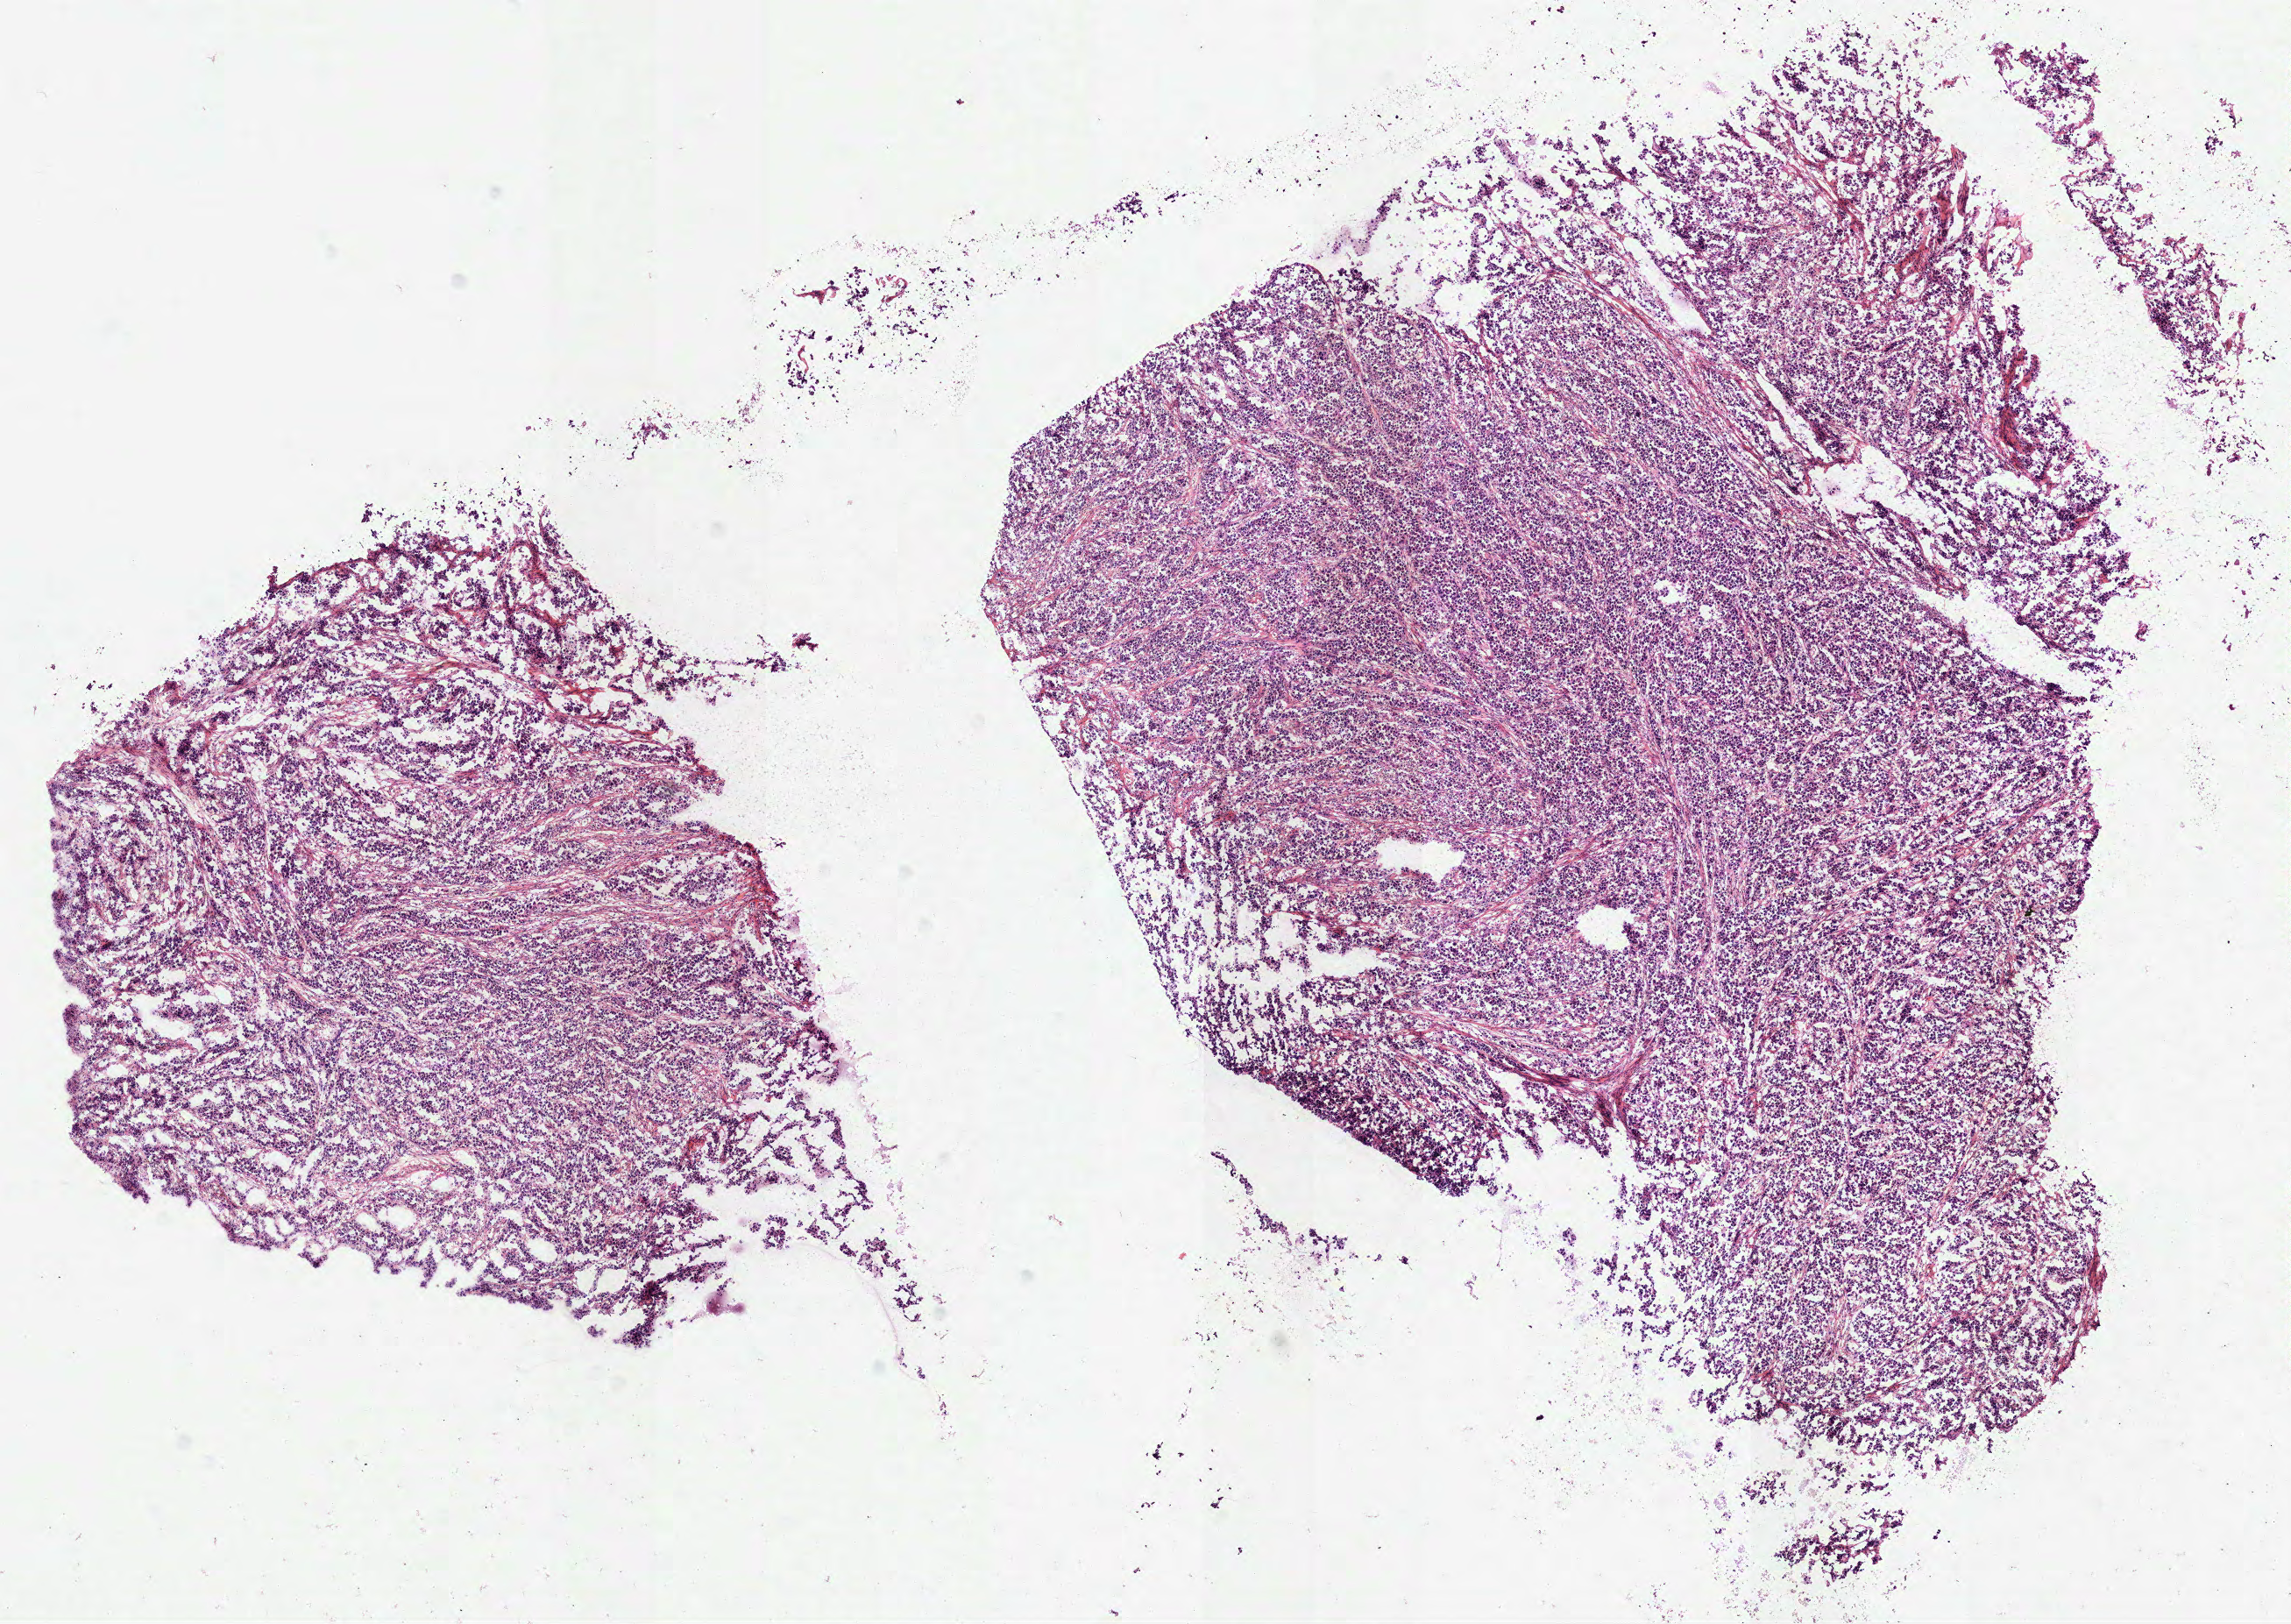
Whole-slide histology image, Hematoxylin and eosin (H&E) stained, low-resolution overview of the scanned area, about 10.5 x 7.5 mm (slide scanned at 40x), frozen section from the top of the tissue portion, sample: primary tumour, stomach. Patient: female, age at initial diagnosis 43 years. Histologic grade: G3 (poorly differentiated). Composition of this section per pathologist review: tumour cells 90%, tumour nuclei 85%, normal cells 0%, stromal cells 10%, necrosis 0%.
Diagnosis: Adenocarcinoma, NOS (gastric antrum). AJCC pathologic stage: IIIA (6th edition).